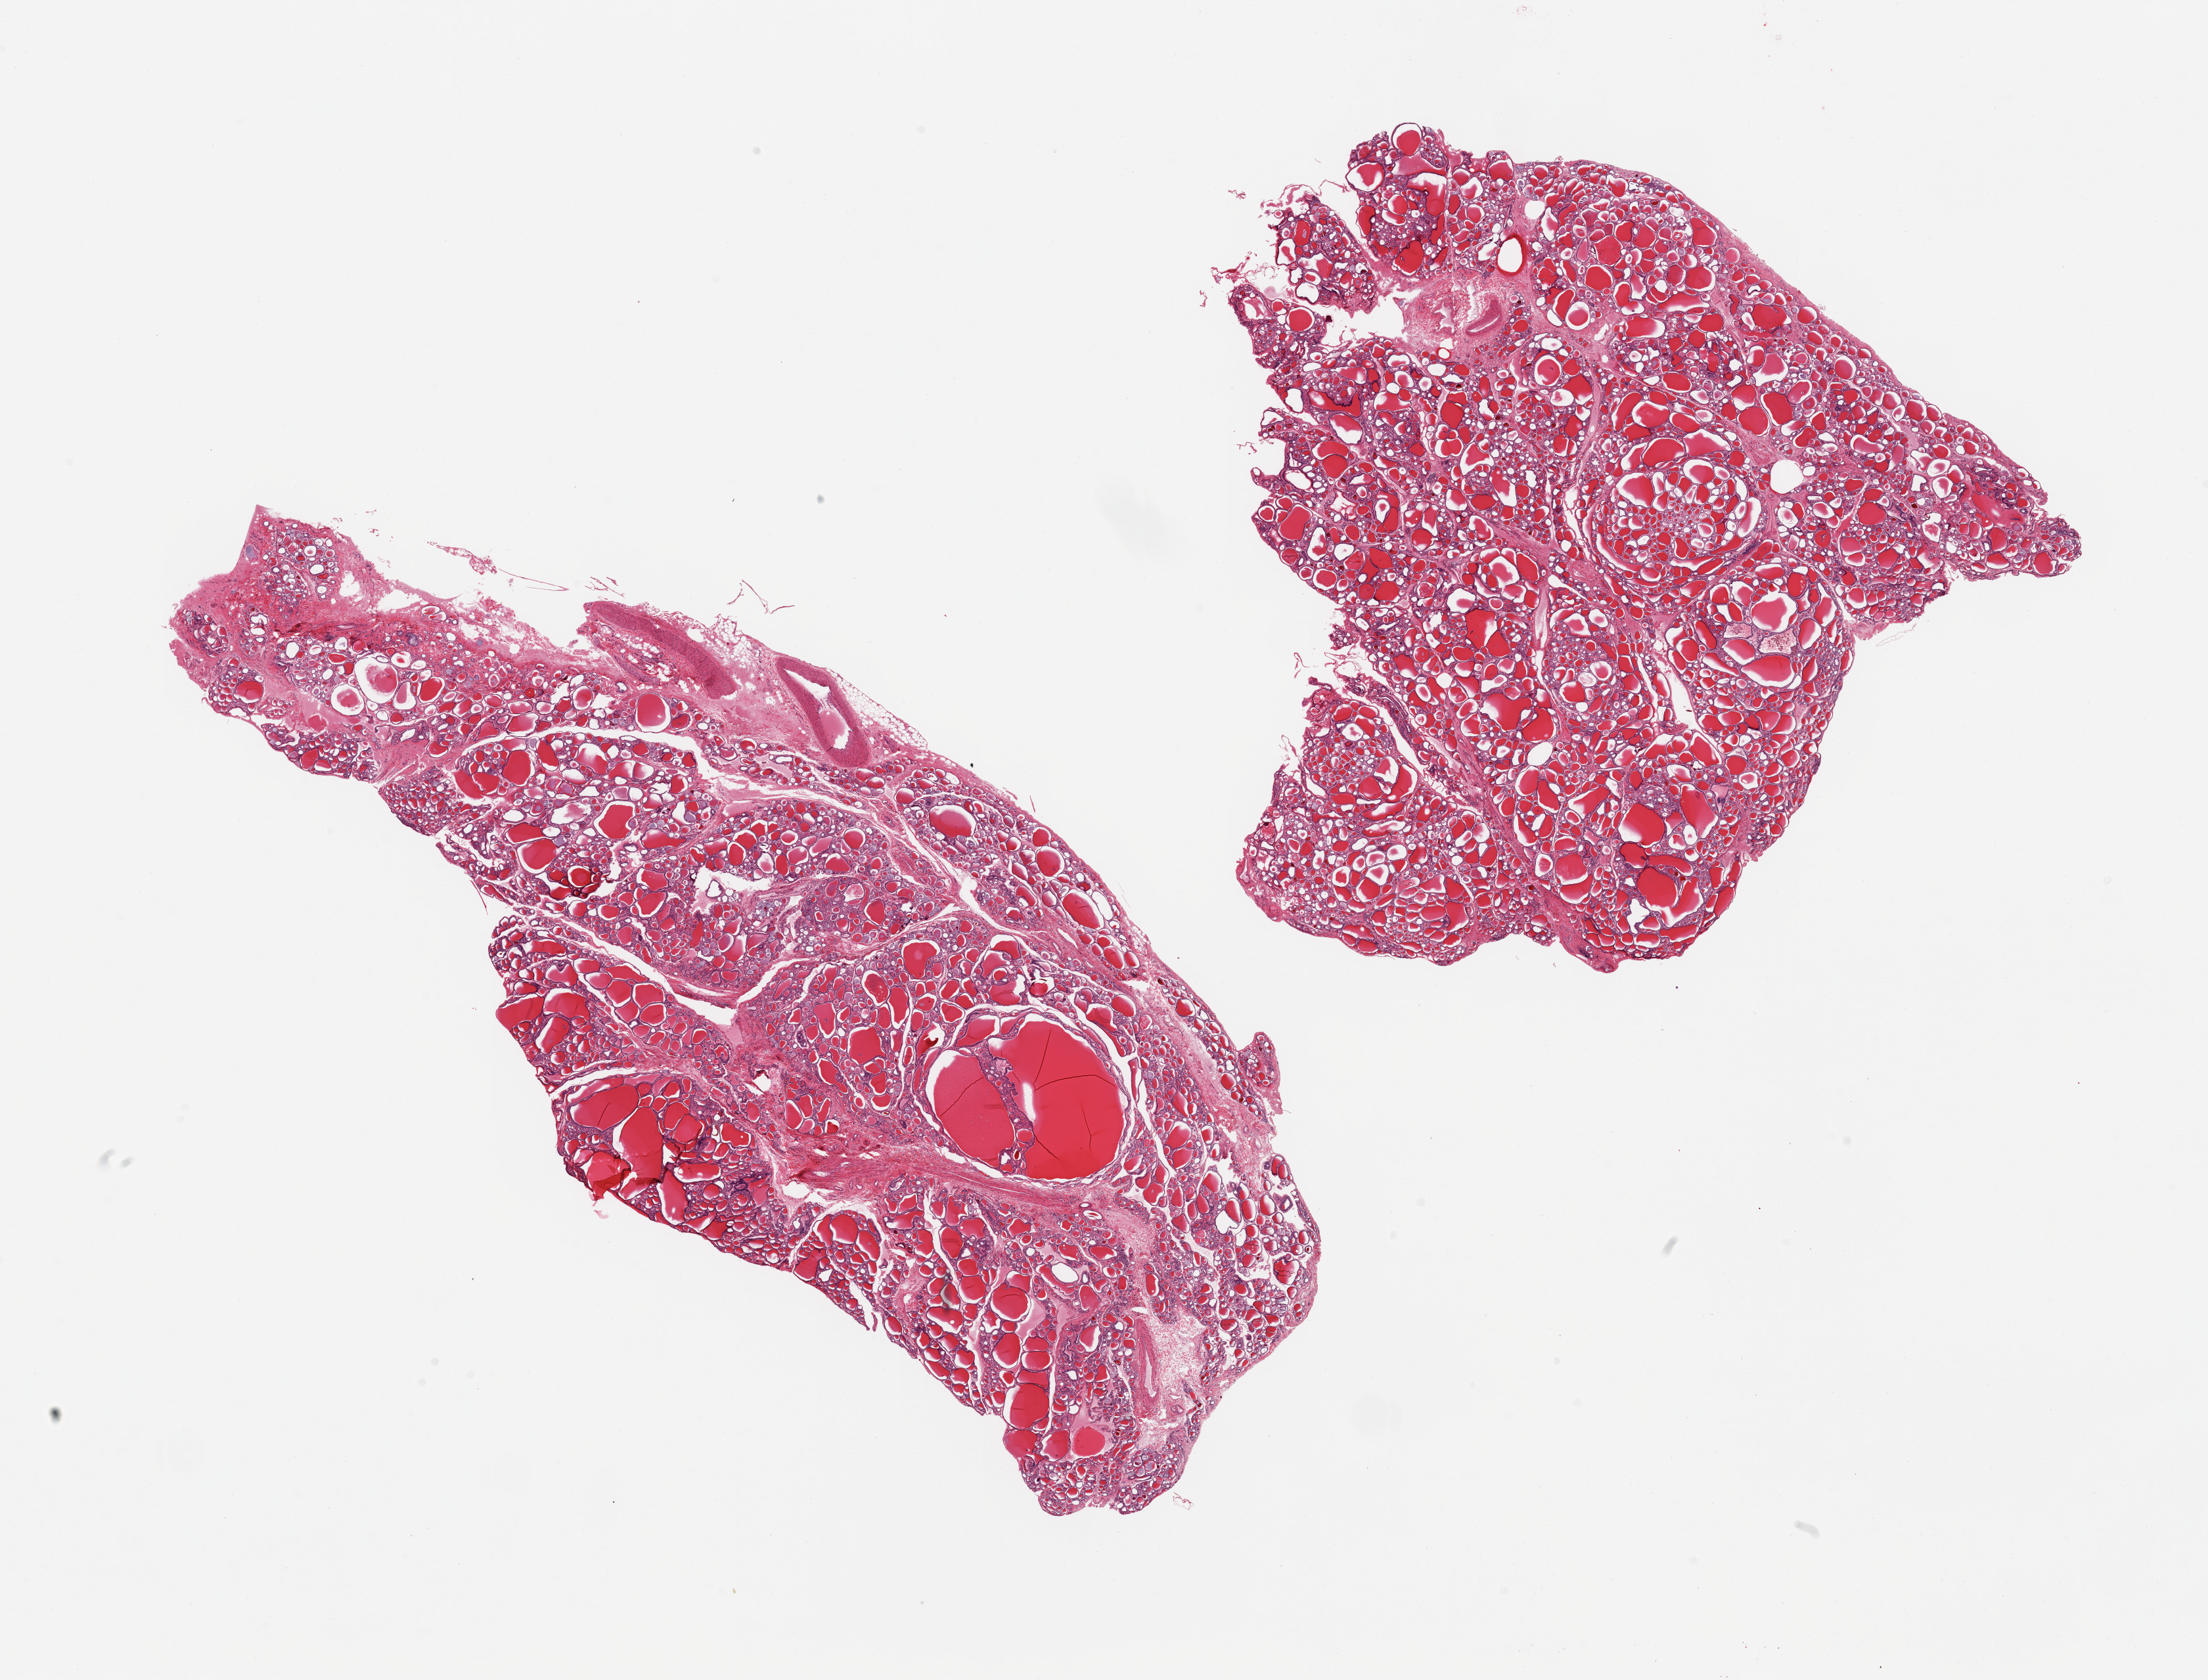
Digitized haematoxylin and eosin-stained section, brightfield — low-resolution overview of the scanned area, about 26.6 x 20.2 mm. PAXgene-fixed paraffin-embedded (PFPE) section. Target tissue: thyroid. Donor tissue sample. Donor sex: female.
- review note (as recorded): 2 pieces, incidental 2mm colloid cyst, no abnormalities